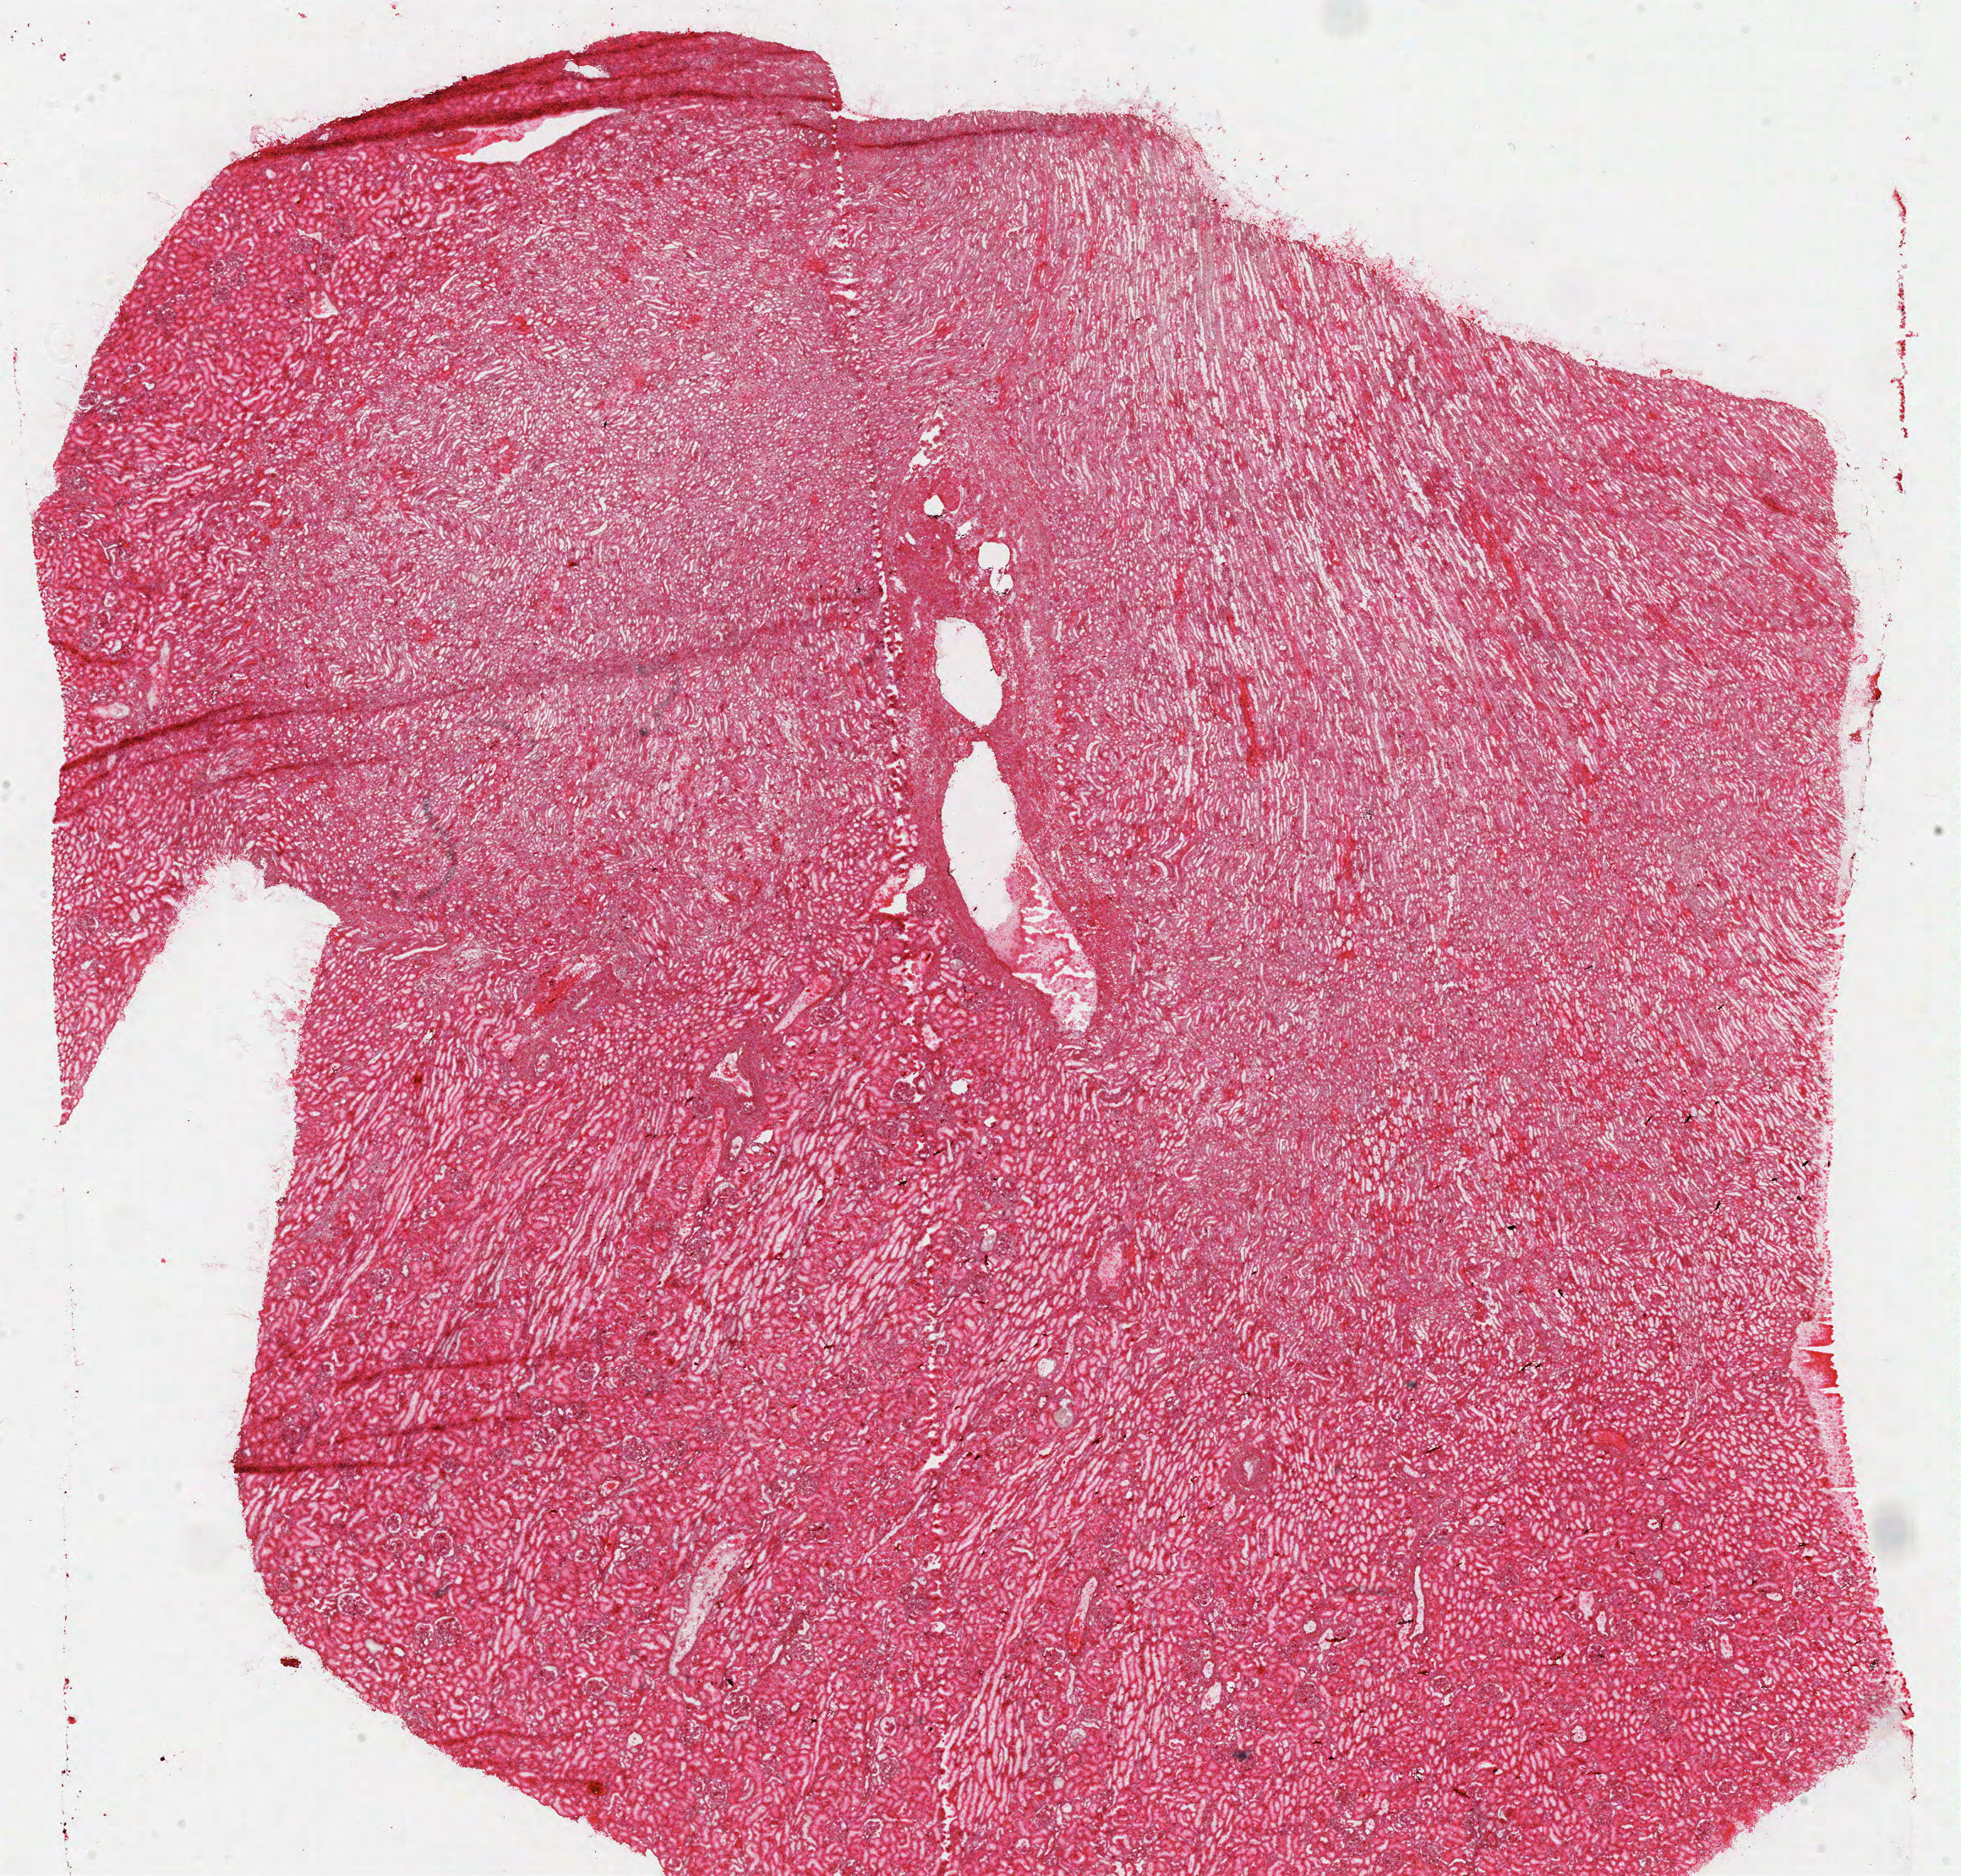
H&E-stained whole-slide image, low-resolution overview of the scanned area, about 18.3 x 17.5 mm. Frozen section from the top of the tissue portion. Sample: solid tissue normal (non-tumour tissue), kidney. Patient: male, age at initial diagnosis 54 years.
This section: solid tissue normal (non-tumour) sample from the same patient. Patient diagnosis: Papillary adenocarcinoma, NOS.